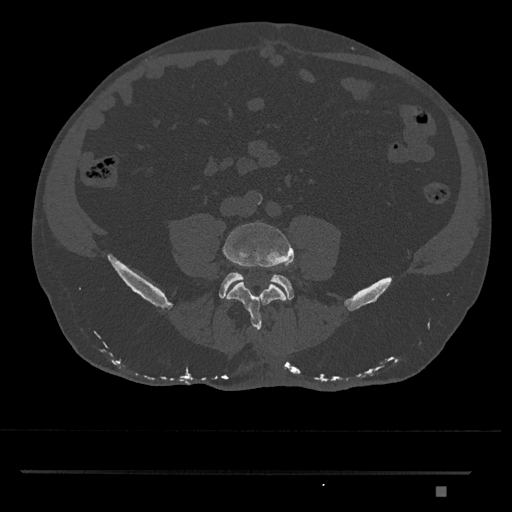
CT including the spine, one axial slice; position 591 of 1134 along the scan axis; reconstruction kernel Br40s/3; 120 kVp; bone window (W 1800 / L 400 HU); 0.5 mm slice thickness; 512 × 512 image matrix, field of view 429 × 429 mm. Patient: male, 65 years. Case-level facts recorded for this patient, not image findings: primary cancer: prostate.
Outlined on this slice (semi-automatic segmentation, software-assisted and operator-edited):
- L4 vertebra: bounding box (x1, y1, x2, y2) in pixels: (223, 222, 294, 330)
- L5 vertebra: (219, 272, 294, 300)